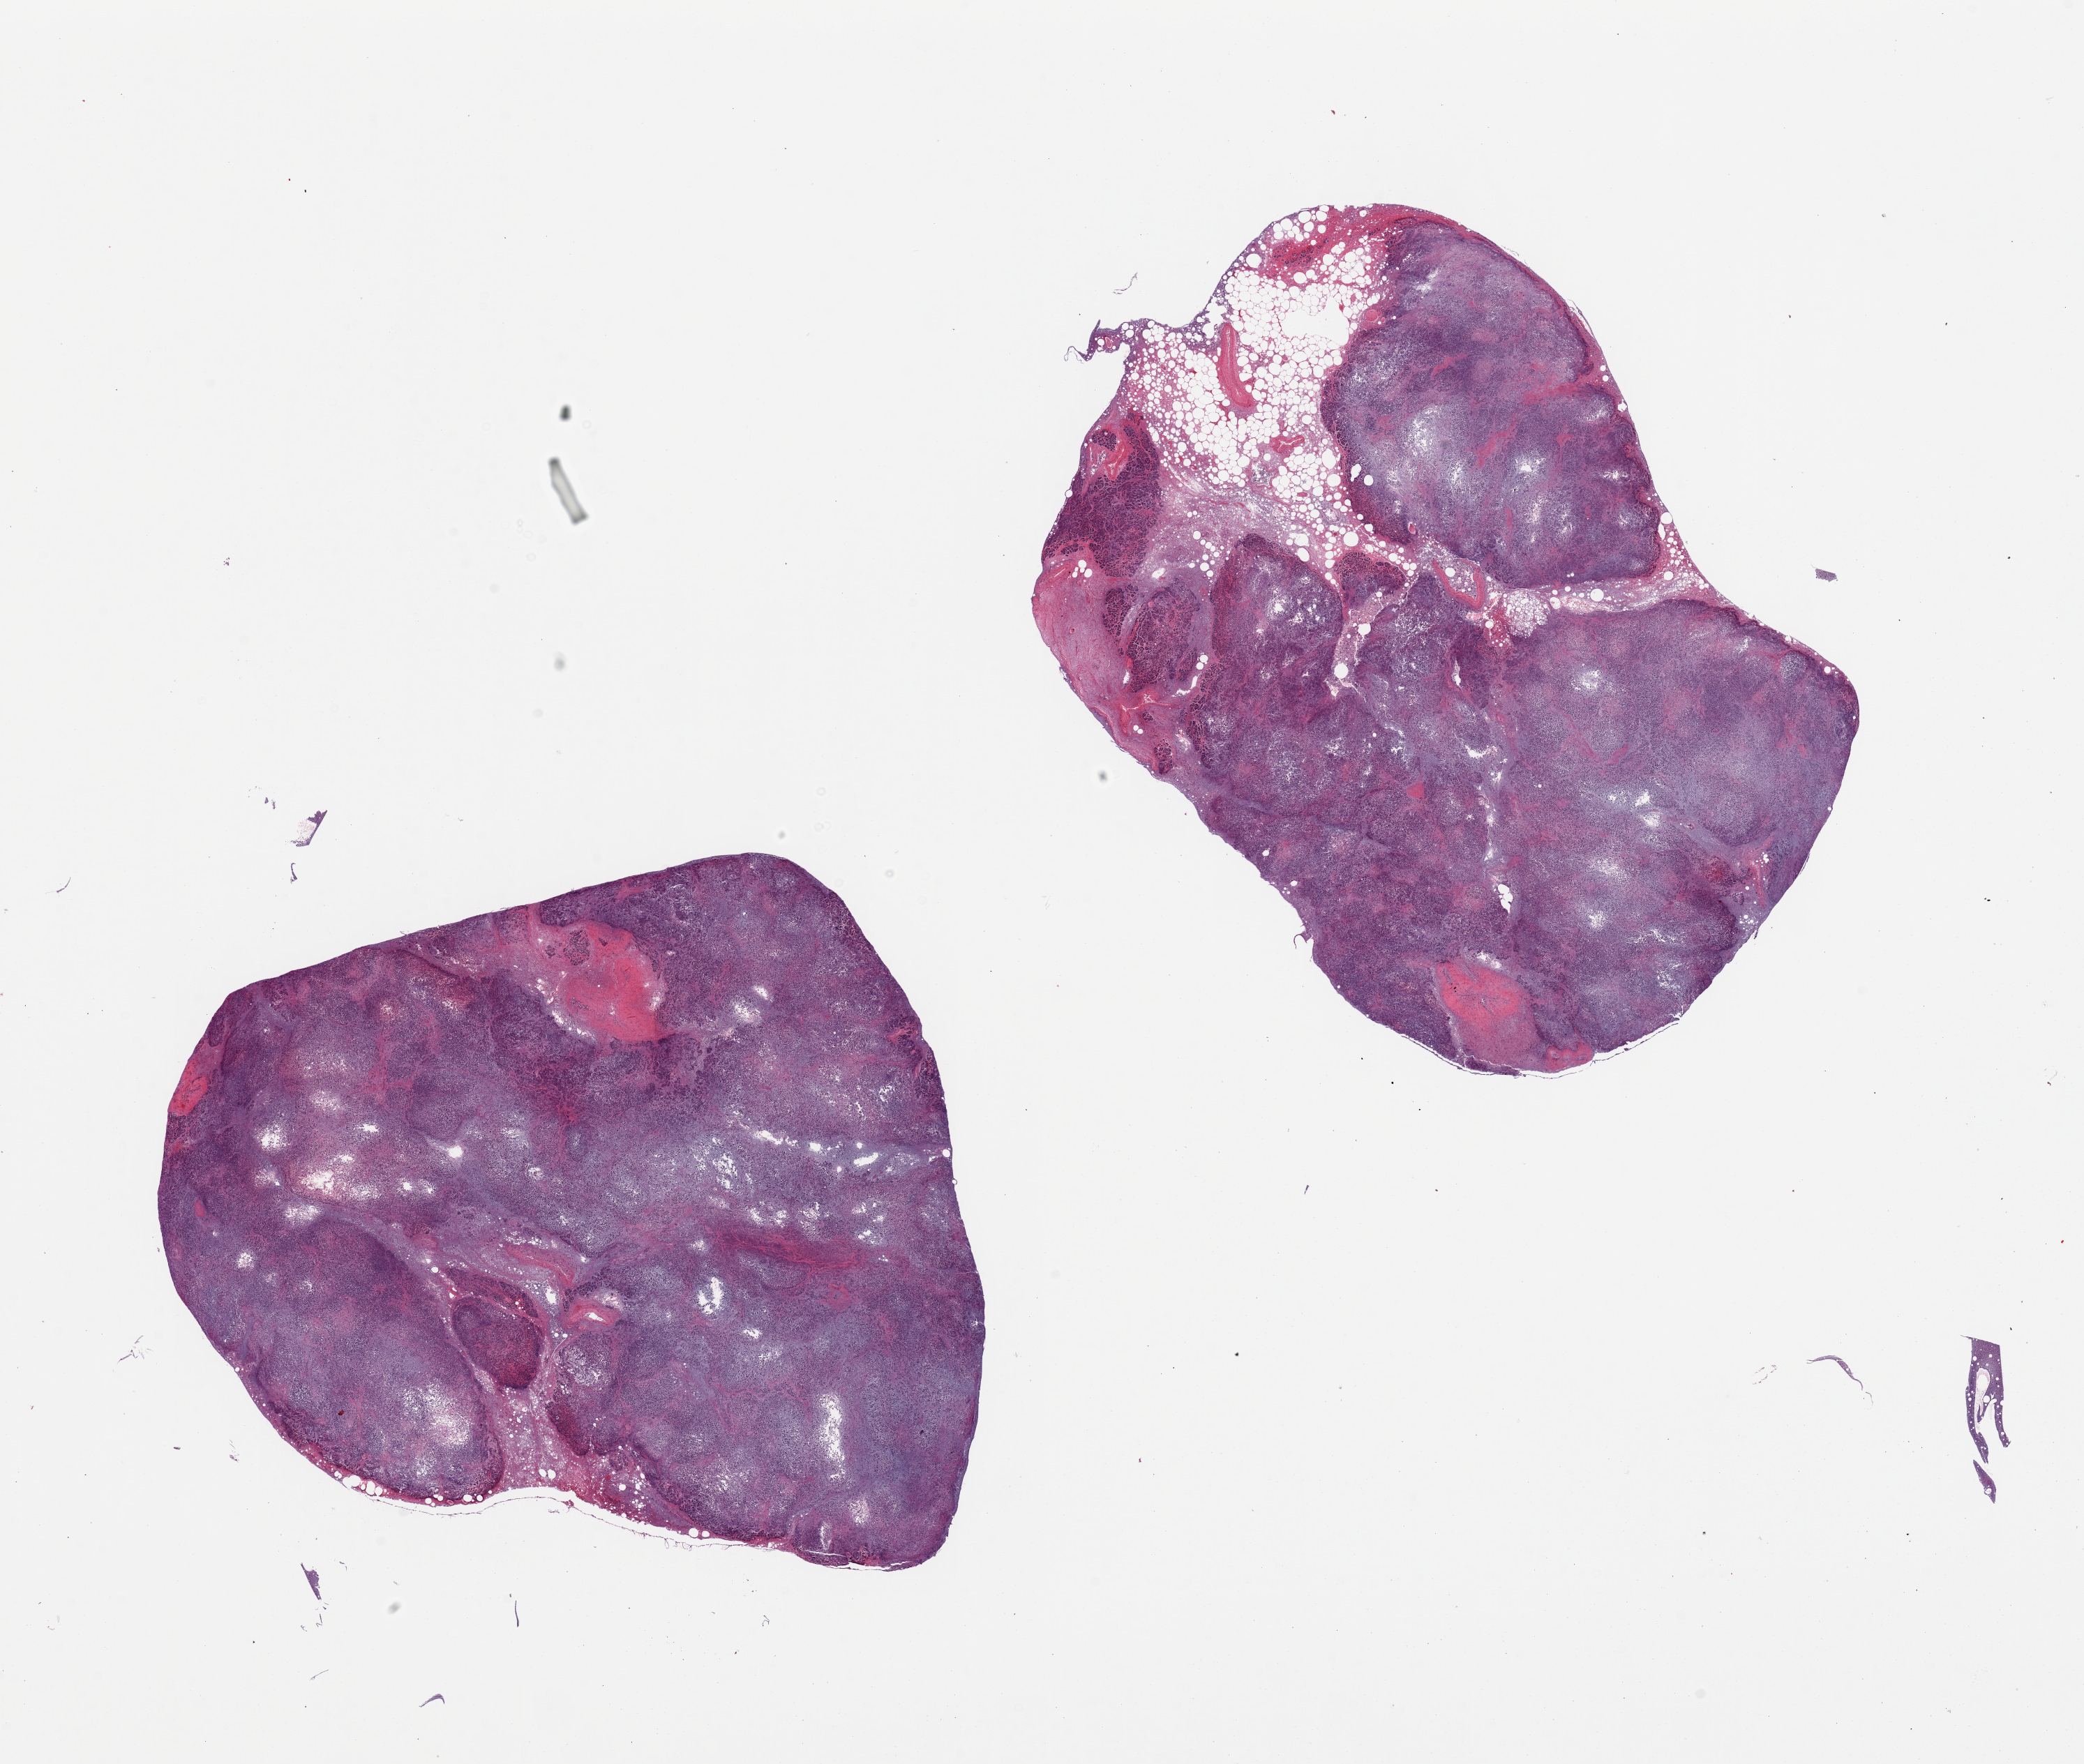
Whole-slide image, hematoxylin and eosin (H&E) stain, brightfield, shown as a low-resolution overview of the whole scanned area (about 23.6 x 20.0 mm), PAXgene-fixed, paraffin-embedded tissue, target tissue: pancreas, tissue donor sample. Male donor.
* pathologist's review note for this sample: 2 pieces. Severely autolyzed